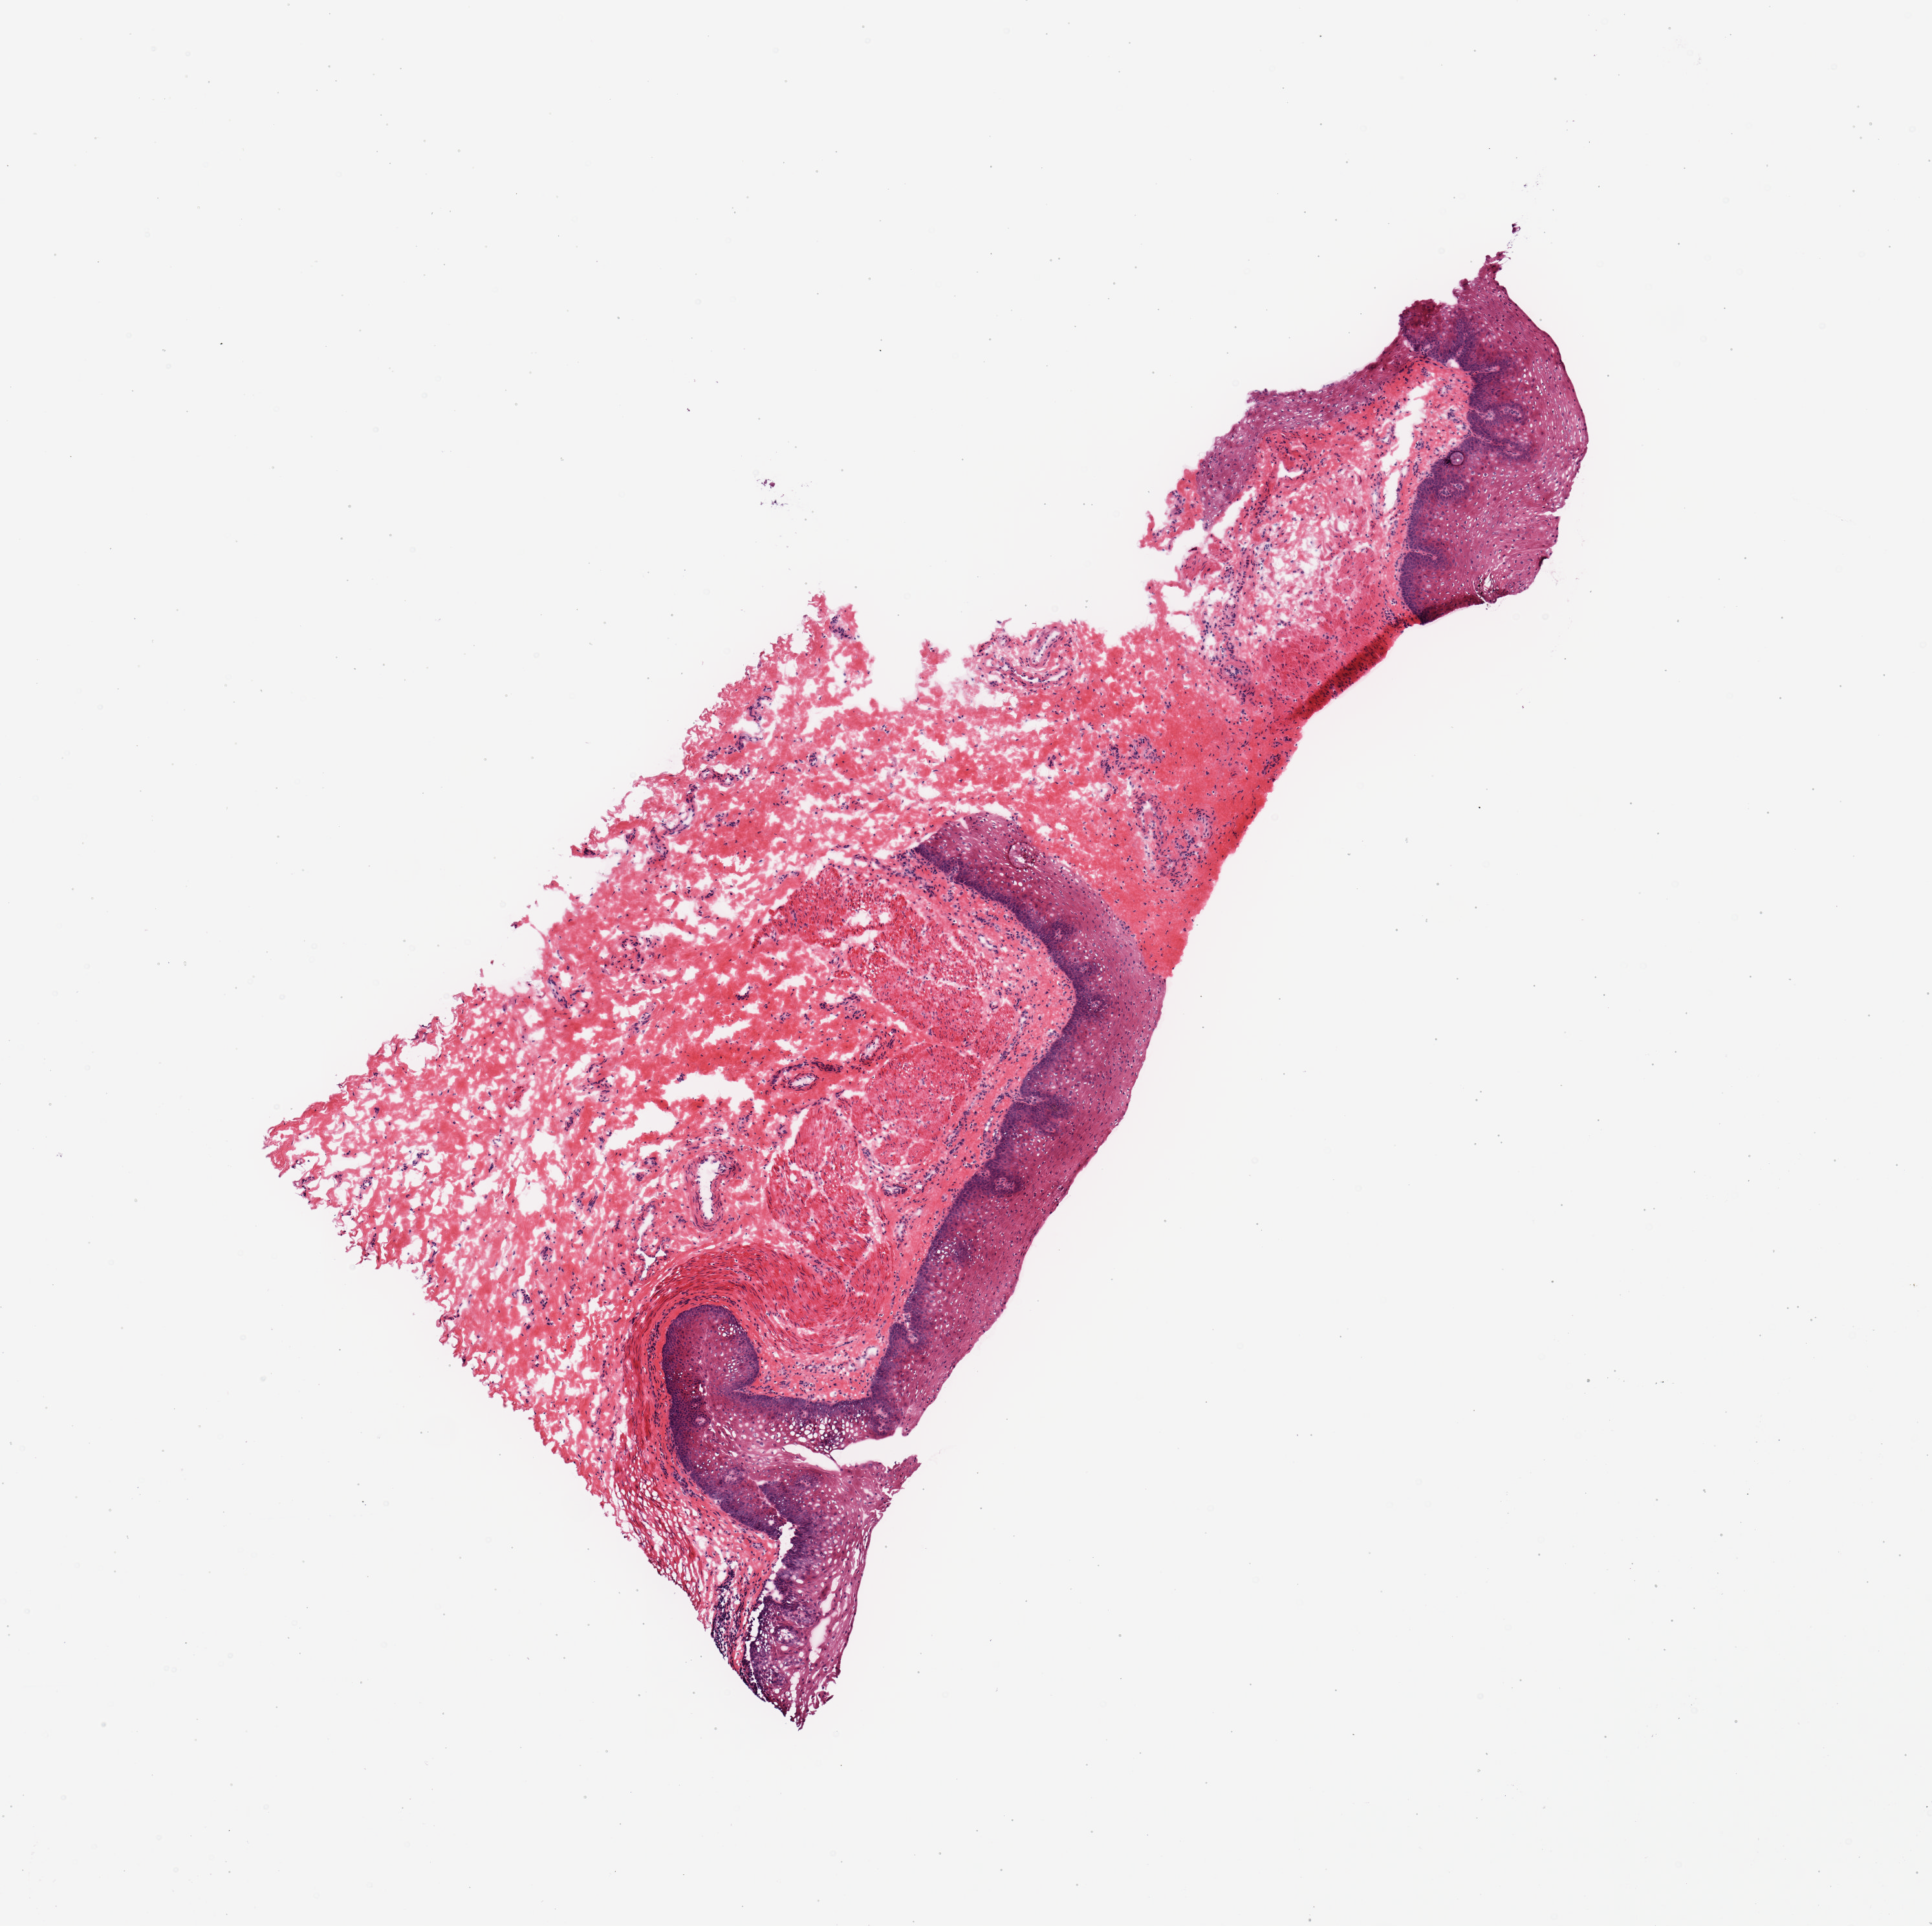
Digitized hematoxylin and eosin (H&E)-stained section, whole scanned area (about 5.9 x 5.9 mm) shown as a low-resolution overview. Frozen section (dry ice). Sampled site (target tissue): esophageal mucous membrane. Donor tissue sample. Male donor.
Reviewer comment on this tissue sample: 1 piece.